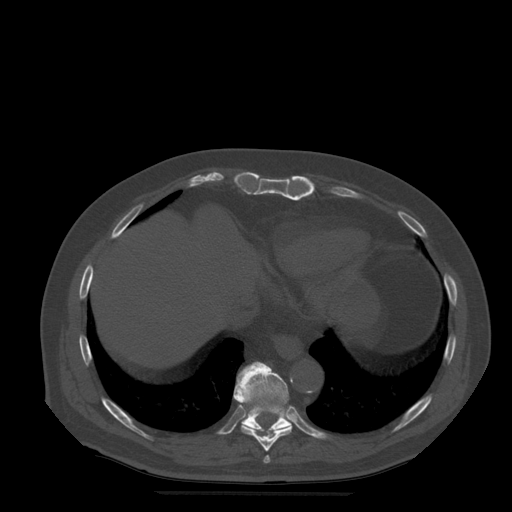
CT including the spine, one axial slice; slice 280 of 522 in the series (ordered by position); bone window (W 1800 / L 400 HU); 1.25 mm slice thickness; 512 × 512 image matrix, field of view 420 × 420 mm. Patient age 72 years. Case-level facts recorded for this patient, not image findings: primary cancer: prostate.
Outlined on this slice (semi-automatically segmented with operator editing):
- T10 vertebra: bounding box [x1, y1, x2, y2] px = [235, 362, 291, 433]
- T8 vertebra: [264, 456, 270, 464]
- T9 vertebra: [234, 379, 293, 452]